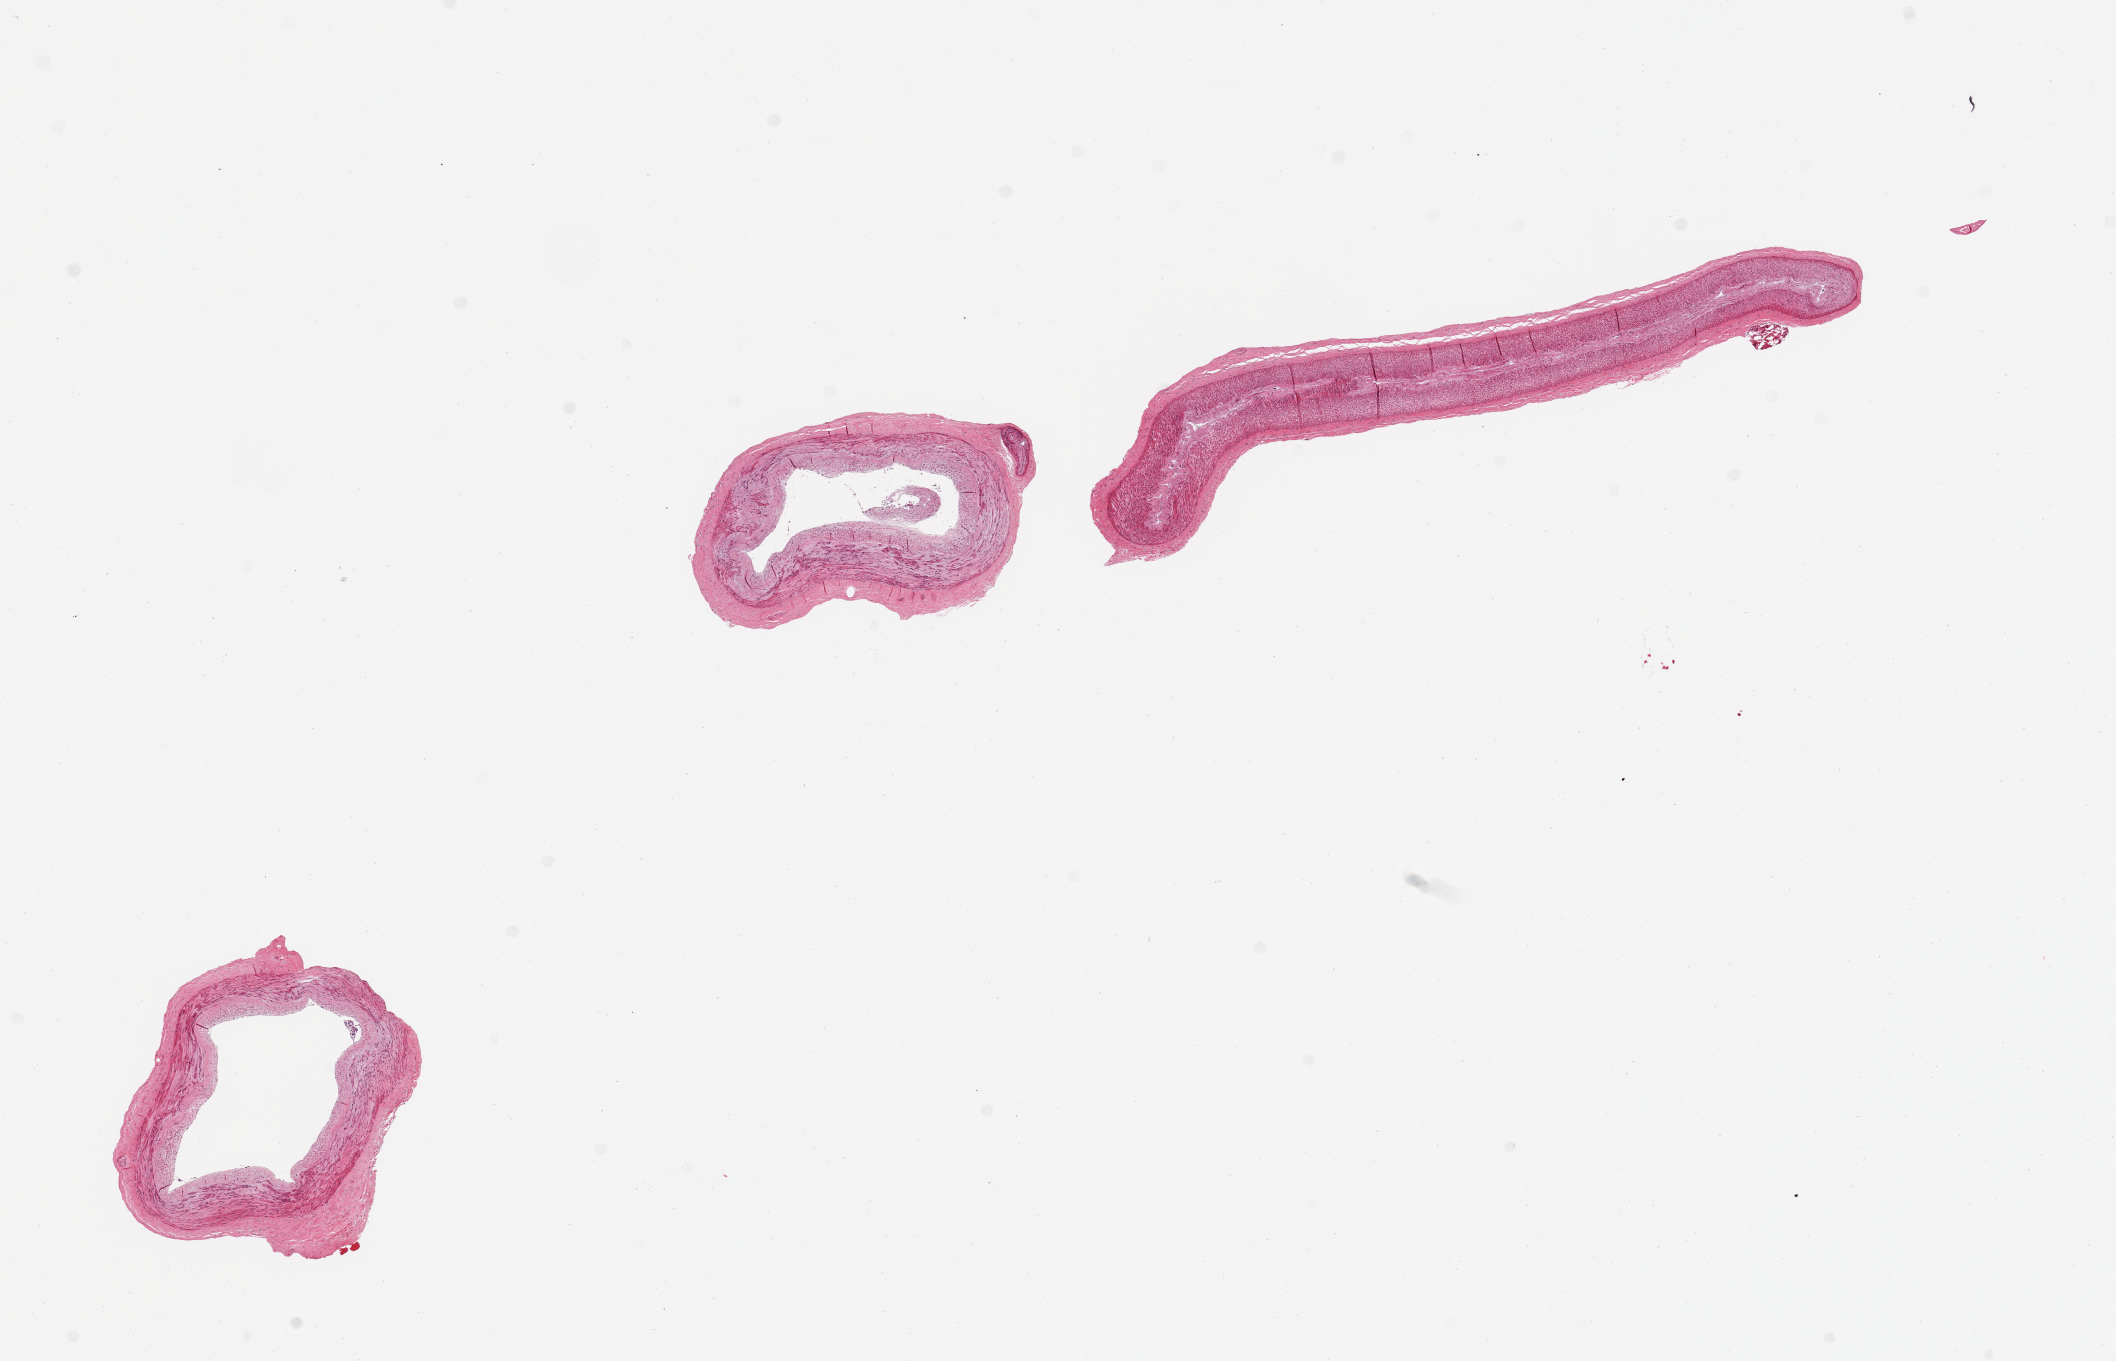
Digitized hematoxylin and eosin (H&E)-stained section, brightfield — whole scanned area (about 16.7 x 10.8 mm, acquisition: 20x scan) shown as a low-resolution overview; PAXgene-fixed, paraffin-embedded tissue; sampled site (target tissue): tibial artery; donor tissue sample.
Reviewer comment on this tissue sample: 3 pieces; well trimmed.